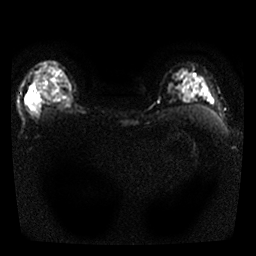
Breast MRI, one axial slice; slice 21 of 25 in the series (ordered by position); diffusion-weighted series; image 2 of 4 stored at this slice position (different b-values; order by instance number); 1.5 T; 256 × 256 image matrix, field of view 300 × 300 mm. Female patient.
Annotated regions visible in this slice (manually delineated by an expert):
- tumour on diffusion-weighted imaging: box from (x=28, y=84) to (x=42, y=116) px